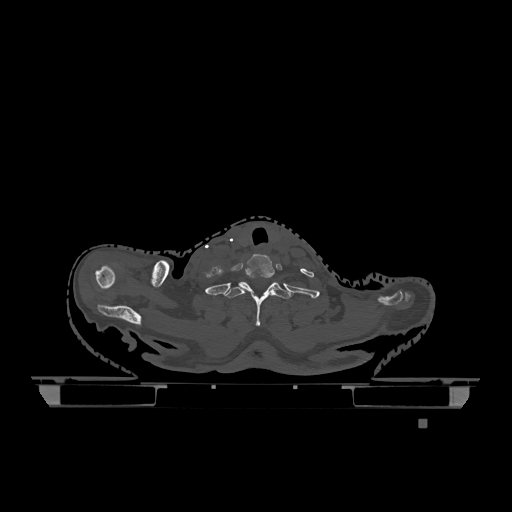
CT including the spine, one axial slice. Position 1010 of 1317 along the scan axis. Bone window (W 1800 / L 400 HU). 512 × 512 image matrix, field of view 500 × 500 mm. Patient: female, 74 years. From the clinical record (not read from this slice): primary cancer: lung.
Structures marked on this image (semi-automatically segmented with operator editing):
- T1 vertebra: bounding box <222,275,292,326> (left, top, right, bottom; pixels)